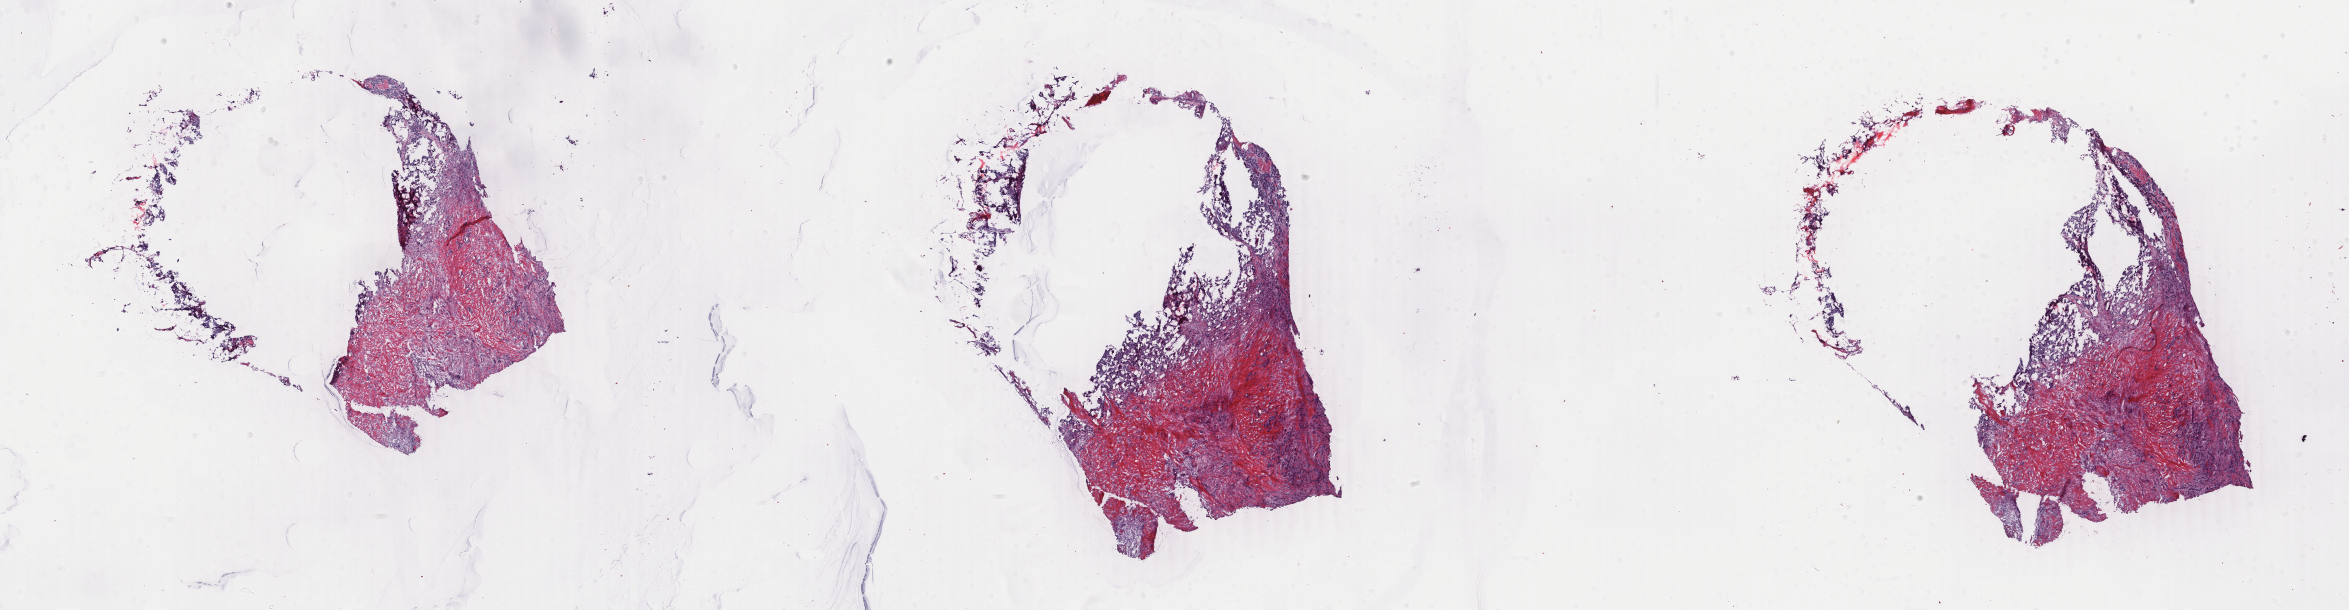
Digitized Hematoxylin and eosin (H&E) stained tissue section (whole slide) — shown as a low-resolution overview of the whole scanned area (about 37.4 x 9.7 mm, slide scanned at 40x); frozen section from the top of the tissue portion; breast, primary tumour sample. Patient: female, age at initial diagnosis 56 years. Composition of this section per pathologist review: tumour cells 70%, tumour nuclei 80%.
Pathologic diagnosis: Infiltrating duct carcinoma, NOS.